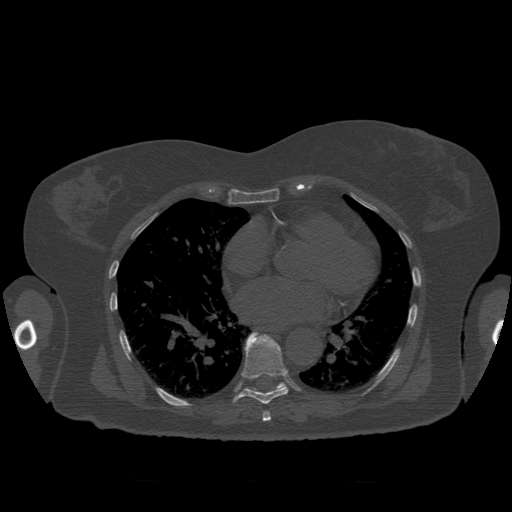
CT including the spine, one axial slice. Slice 375 of 399 in the series (ordered by position). 120 kVp. Bone window (W 1800 / L 400 HU). 512 × 512 image matrix, field of view 404 × 404 mm. Patient age 81 years. Case-level facts recorded for this patient, not image findings: primary cancer: renal; vertebrae with lytic lesions (as recorded): L1.
Annotated regions visible in this slice (semi-automatically segmented with operator editing):
- T7 vertebra: bounding box [x1, y1, x2, y2] px = [263, 411, 272, 421]
- T8 vertebra: [233, 332, 289, 405]
- T9 vertebra: [246, 383, 287, 390]